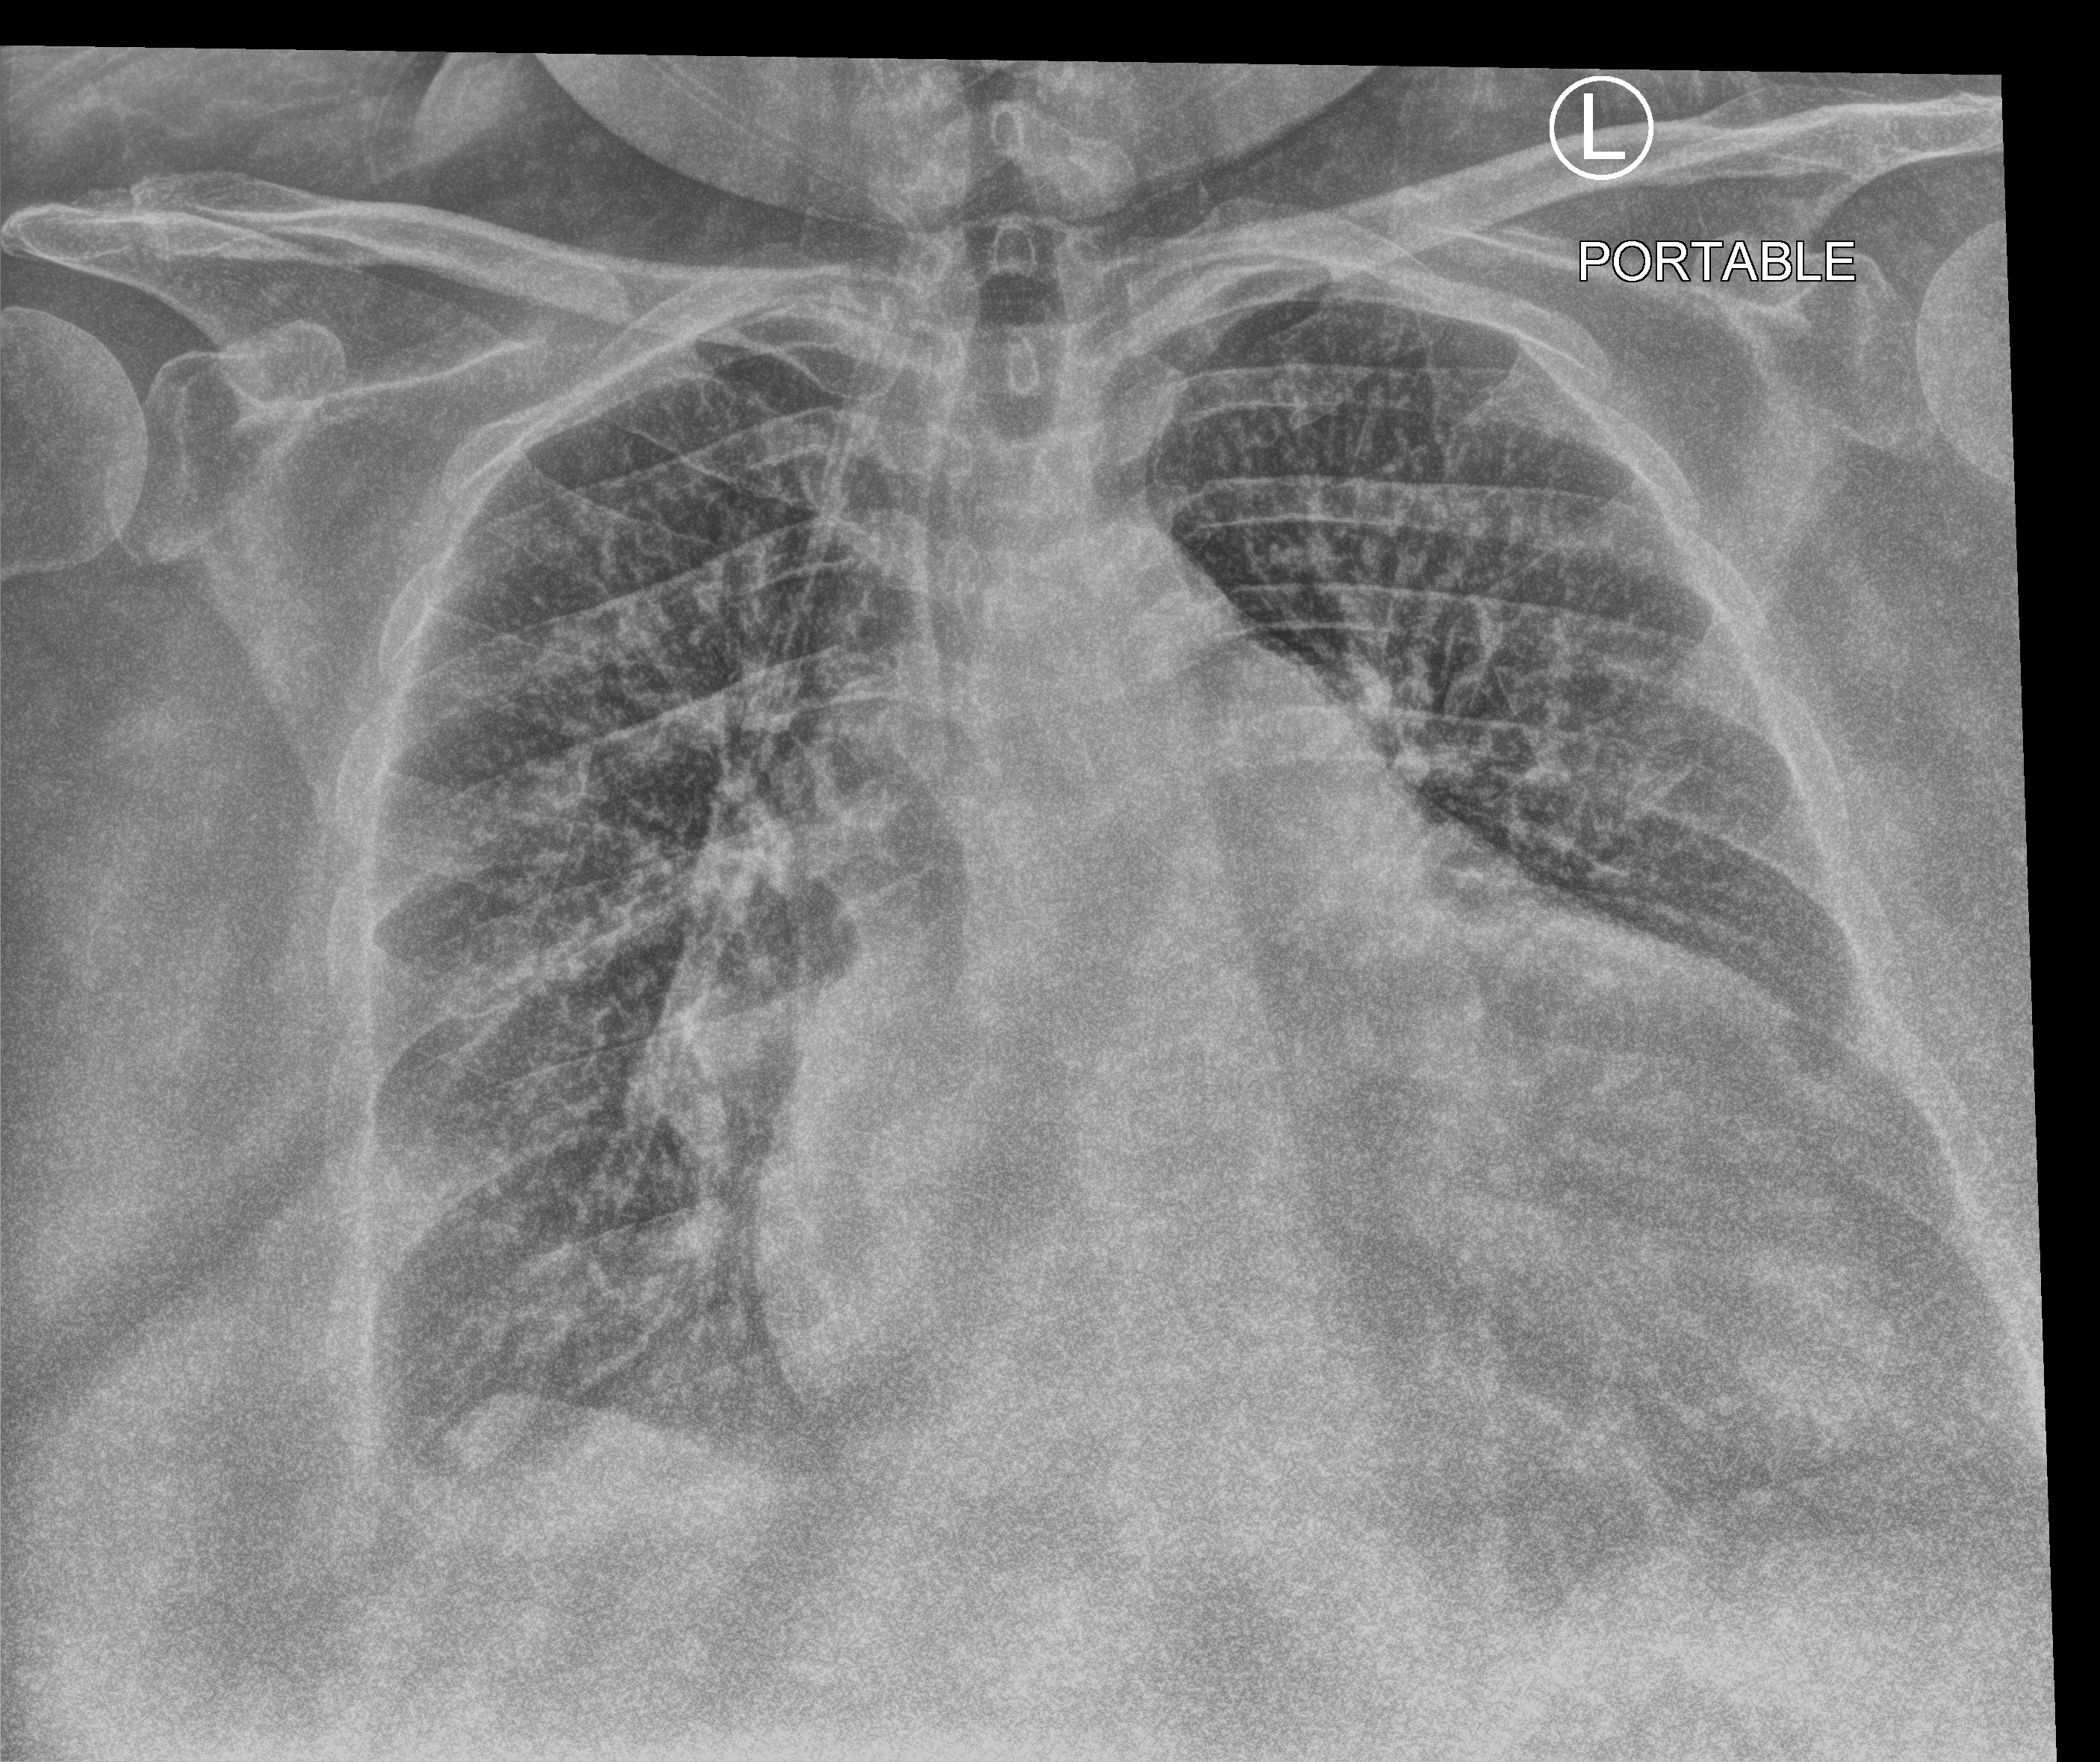
Portable chest radiograph, anteroposterior (AP) projection. Female patient hospitalised with COVID-19, age 60–74 years.
Admission-level facts for this patient (not findings on this image; timing relative to this image not recorded):
- admitted to intensive care during this hospital stay: yes
- other chronic lung disease (admission record): no
- mechanically ventilated during this hospital stay: yes